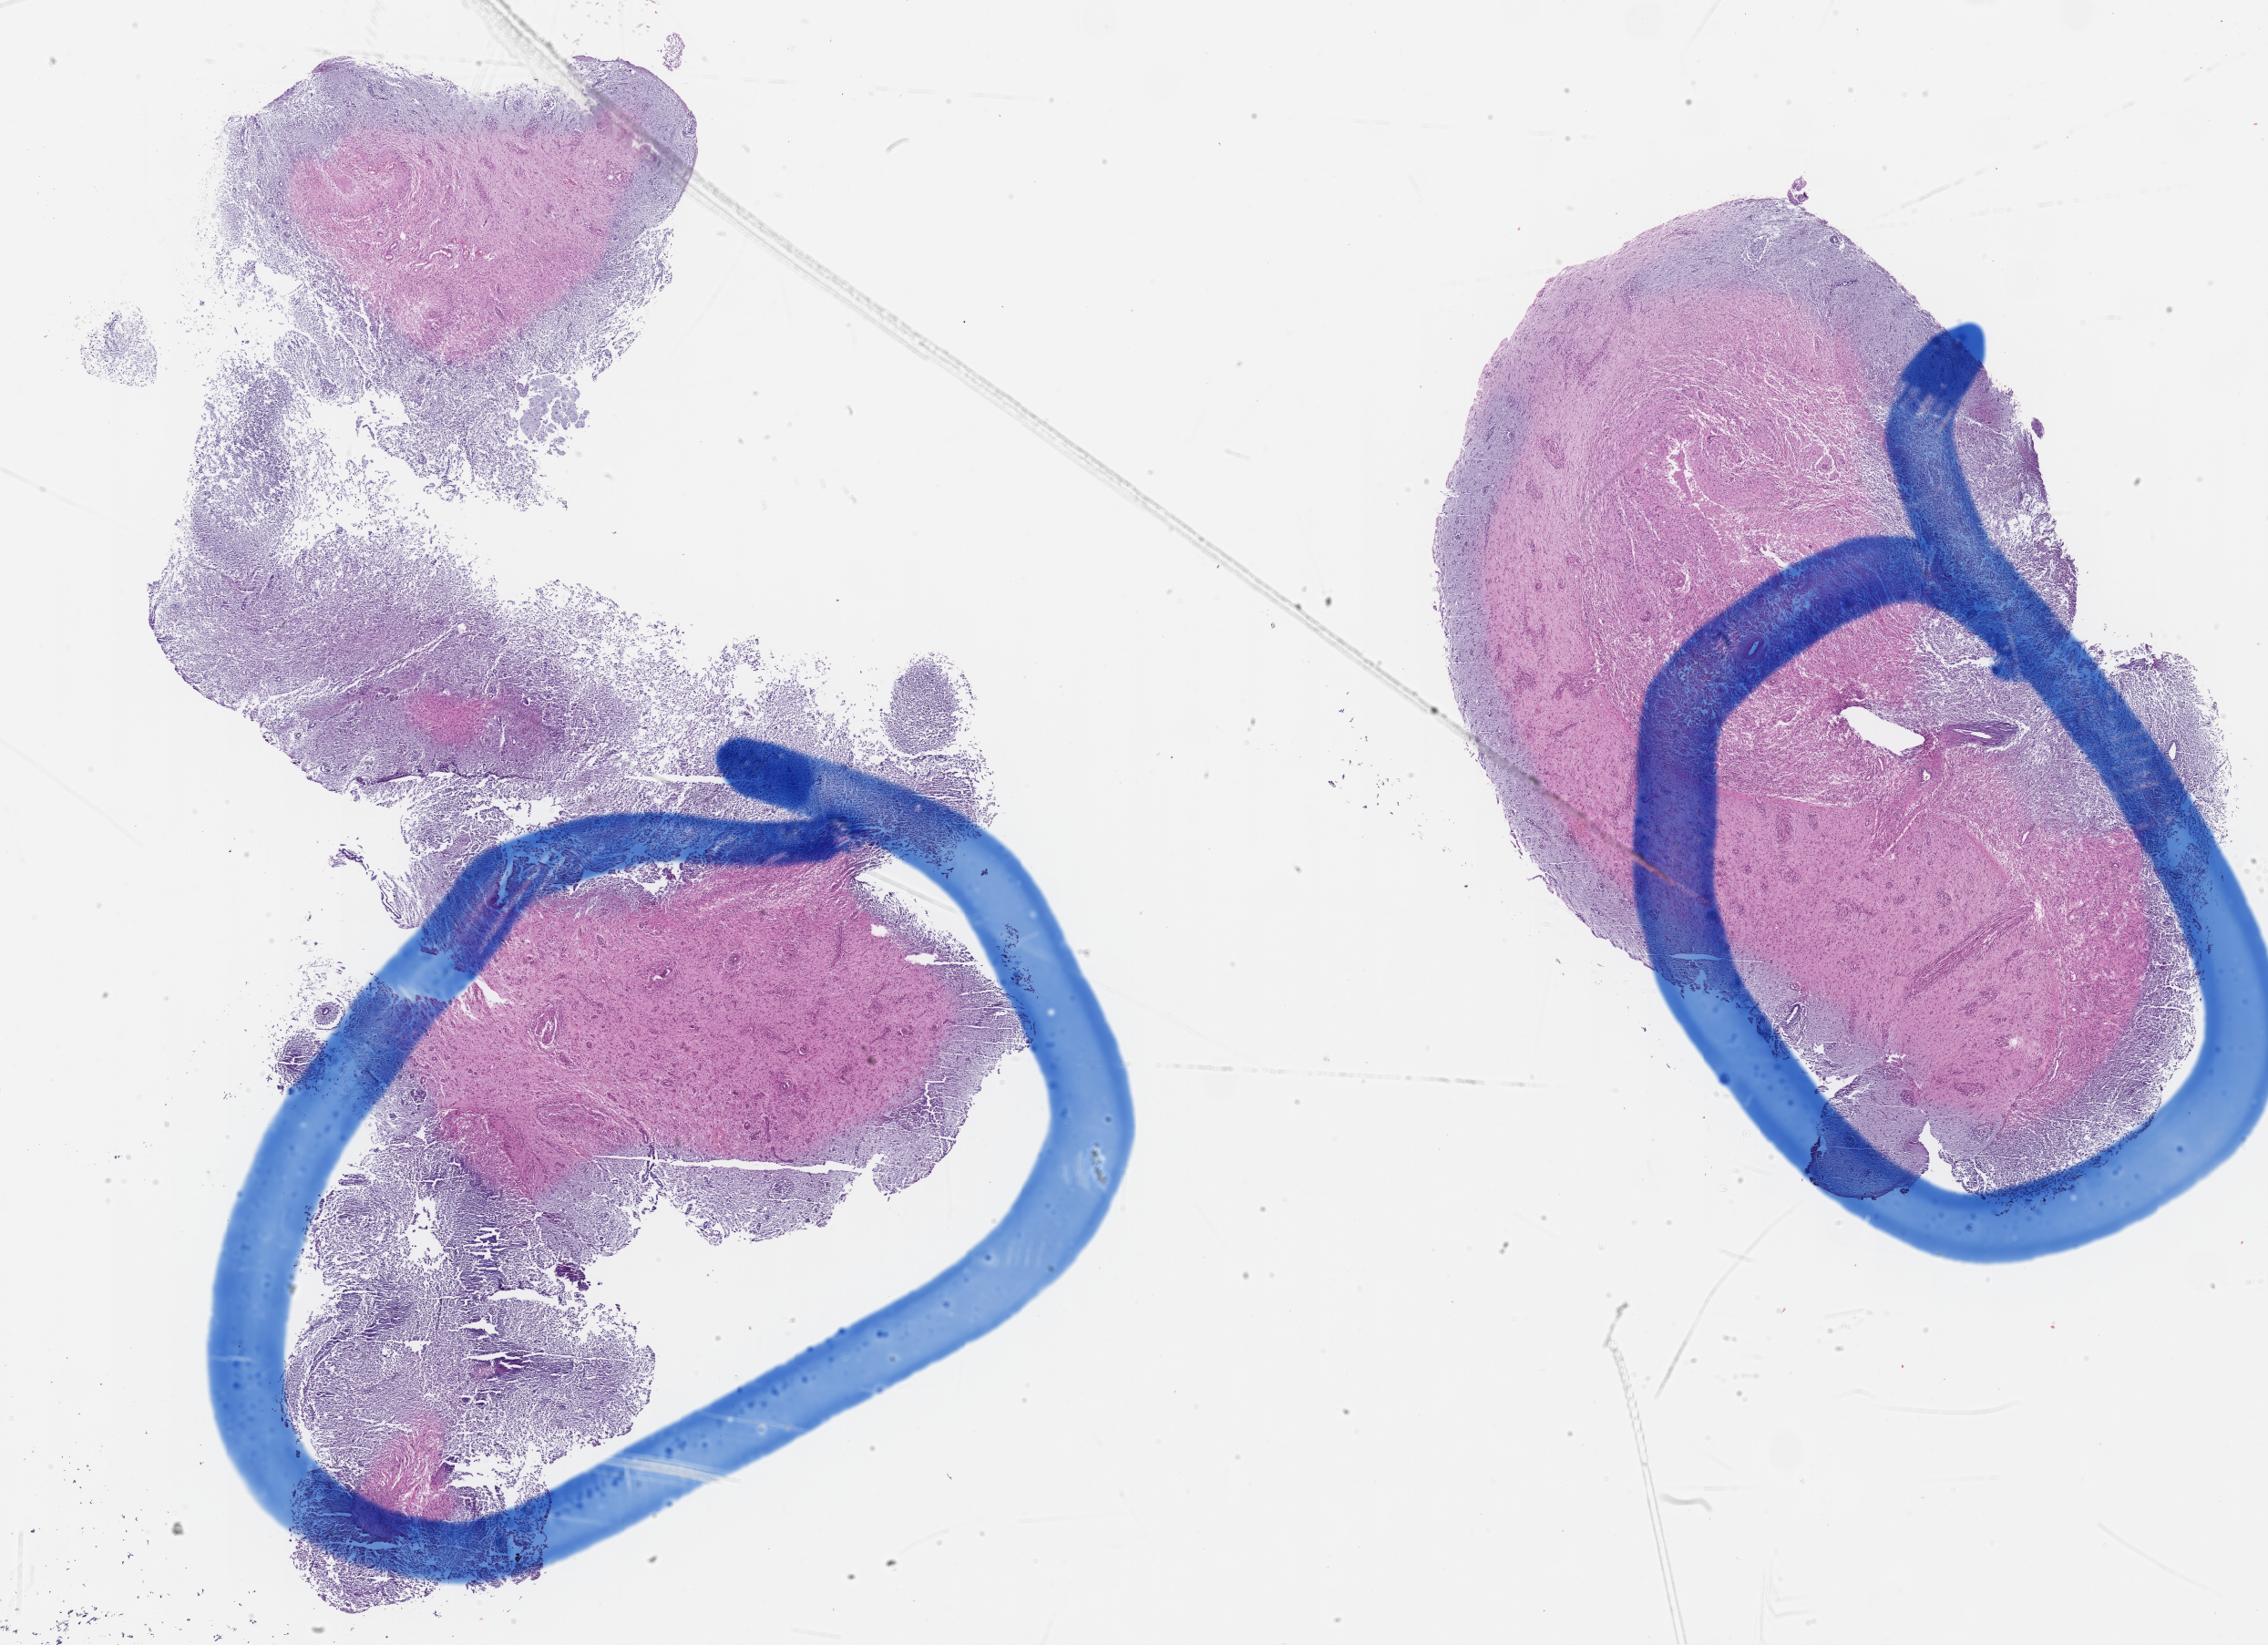
Digitized H&E tissue section (whole slide), low-resolution overview of the scanned area, about 20.2 x 14.6 mm, formalin-fixed paraffin-embedded (FFPE) diagnostic section, sample: primary tumour, brain. Female patient; age at initial diagnosis 82 years.
* pathologic diagnosis: Glioblastoma